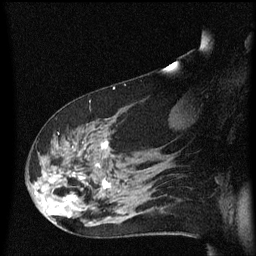
Breast MRI (dynamic contrast-enhanced), one sagittal slice. Slice 37 of 60 in the series (ordered by position). Dynamic contrast-enhanced series, image 2 of 3 at this slice position (ordered by acquisition). 1.5 T. TE 4.2 ms, TR 8.4 ms. 2 mm slice thickness. 256 × 256 image matrix, field of view 200 × 200 mm. Female patient, age 48 years.
Annotated regions visible in this slice (semi-automatic segmentation, software-assisted and operator-edited):
- analysis volume of interest (the breast-tissue region the enhancement analysis was run in; not a lesion): bounding box (x1, y1, x2, y2) in pixels: (31, 116, 134, 225)
- tumour enhancement mask (voxels above the 70 % enhancement threshold inside the analysis volume of interest): (63, 142, 110, 201)